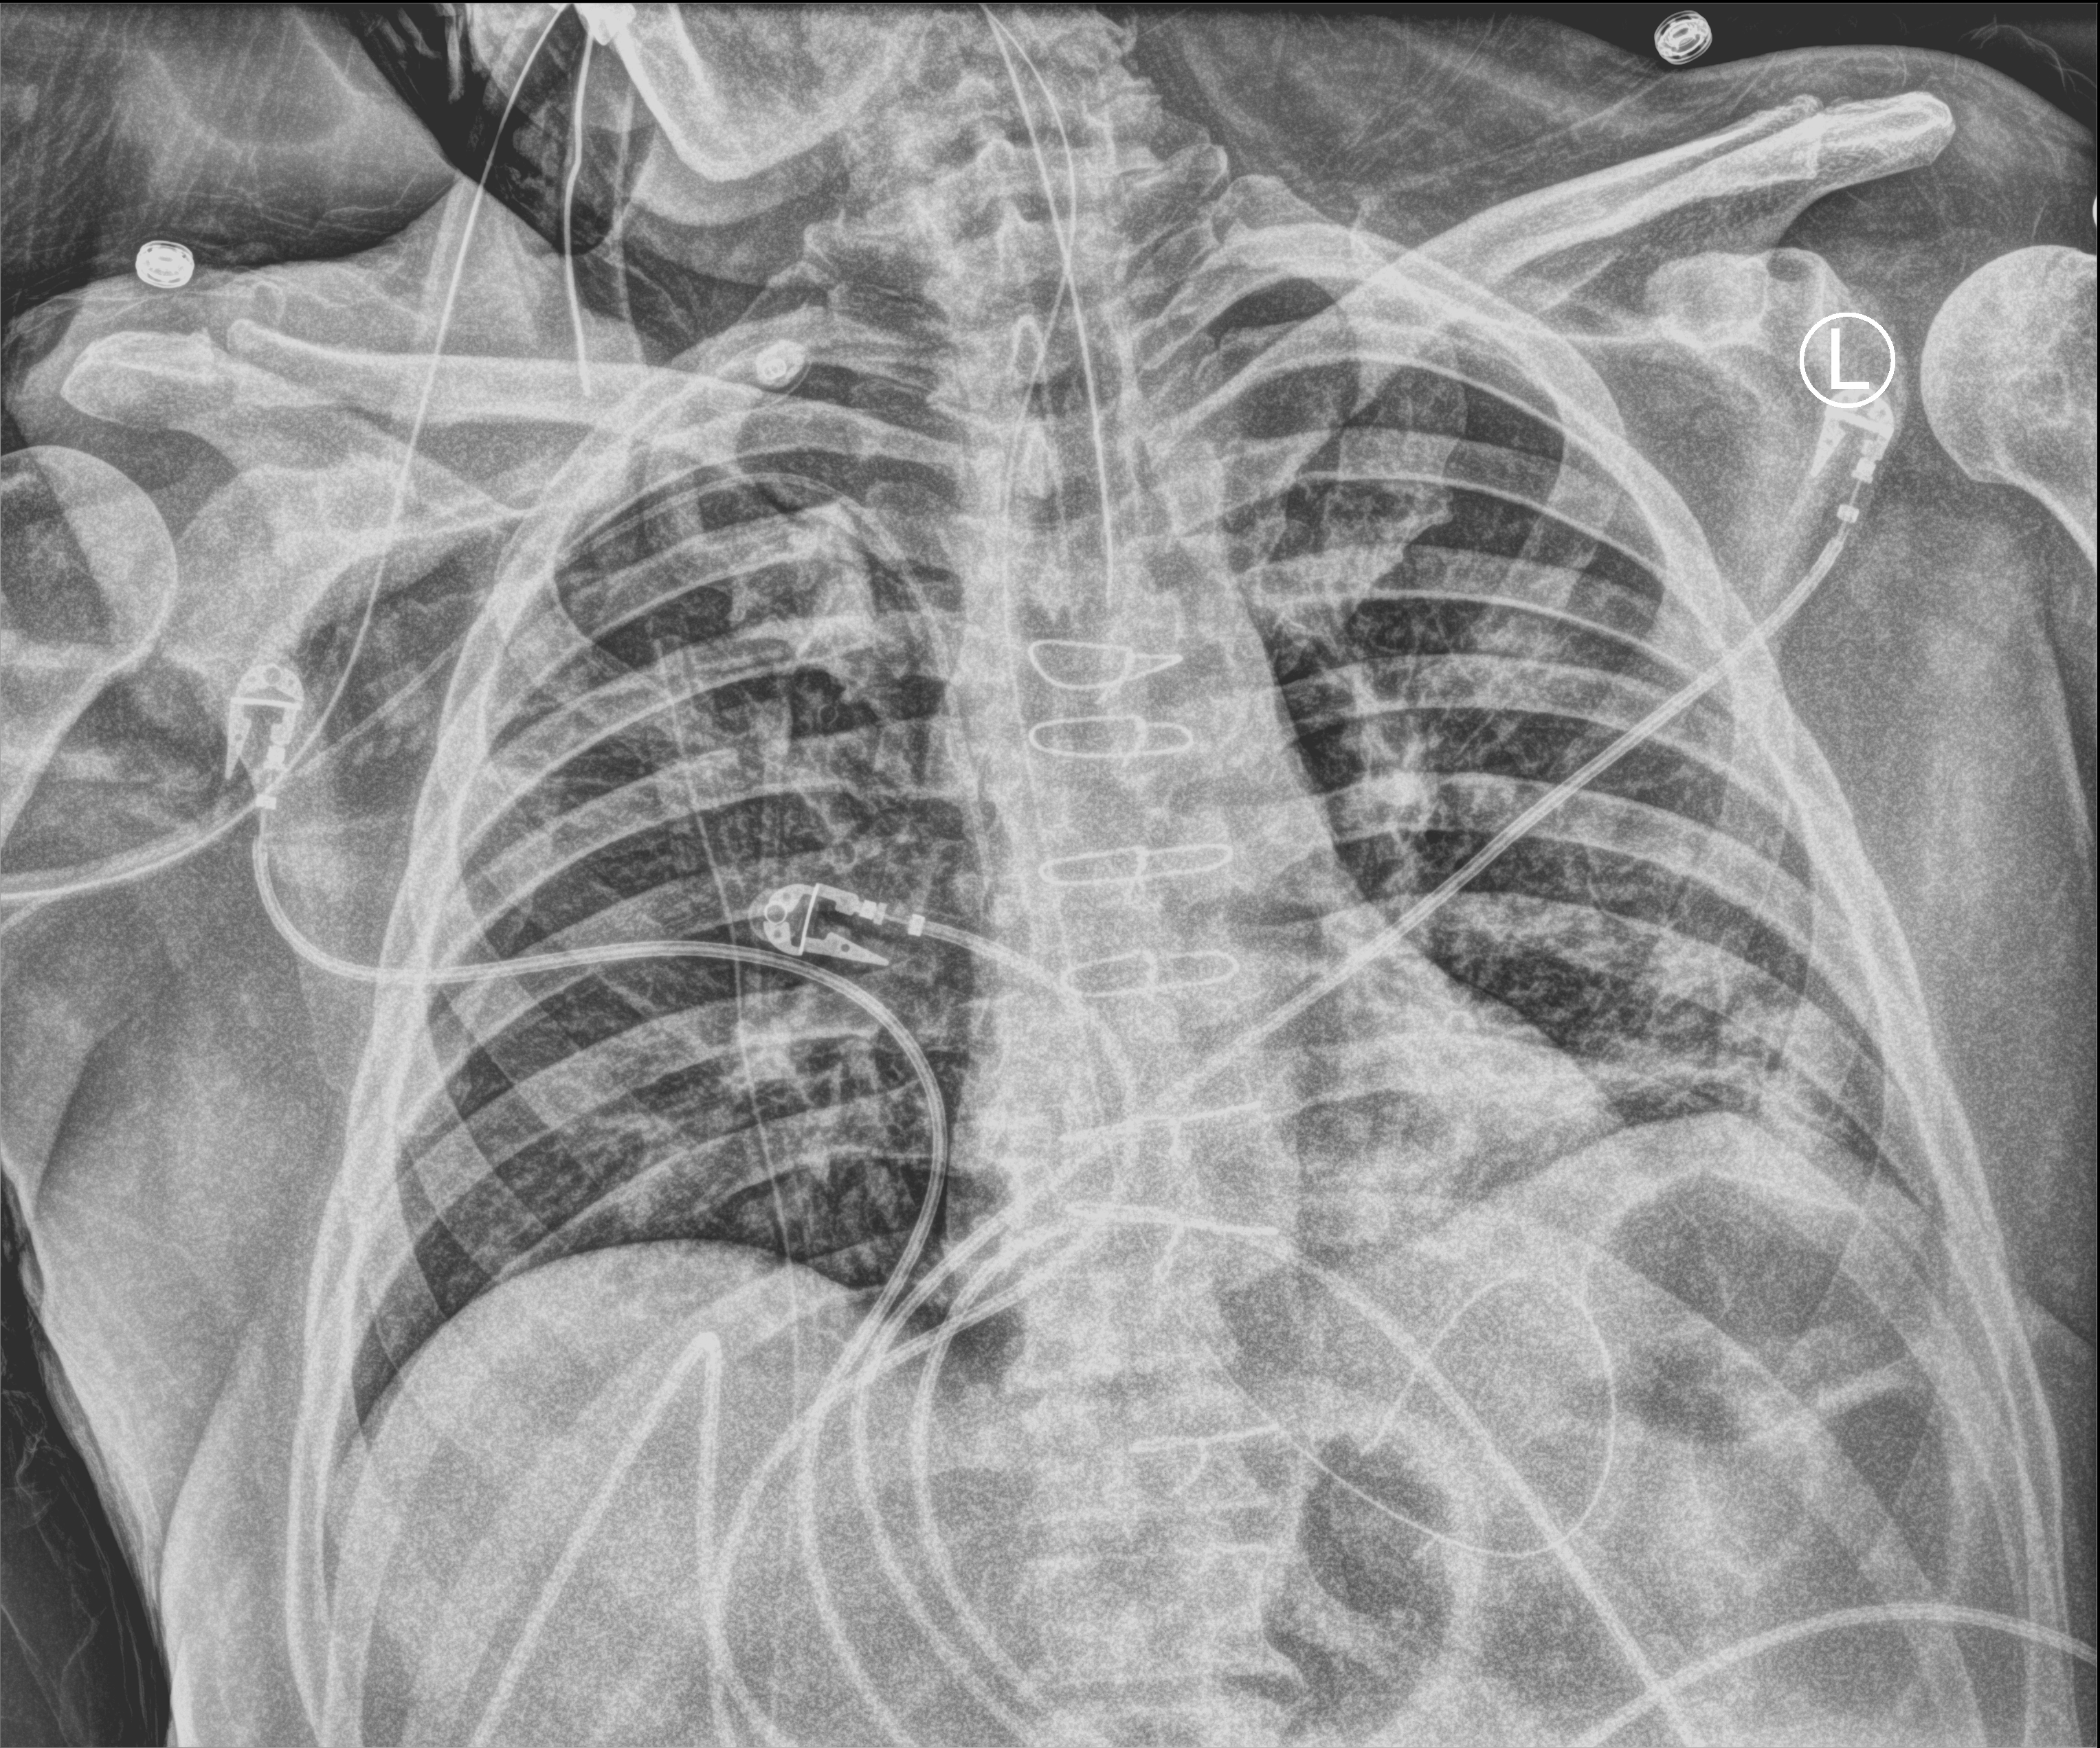
Chest X-ray (portable), anteroposterior (AP) projection. Male patient hospitalised with COVID-19, age 60–74 years.
Admission-level facts for this patient (not findings on this image; timing relative to this image not recorded):
- hypertension (admission record): yes
- mechanically ventilated during this hospital stay: yes
- admitted to intensive care during this hospital stay: yes